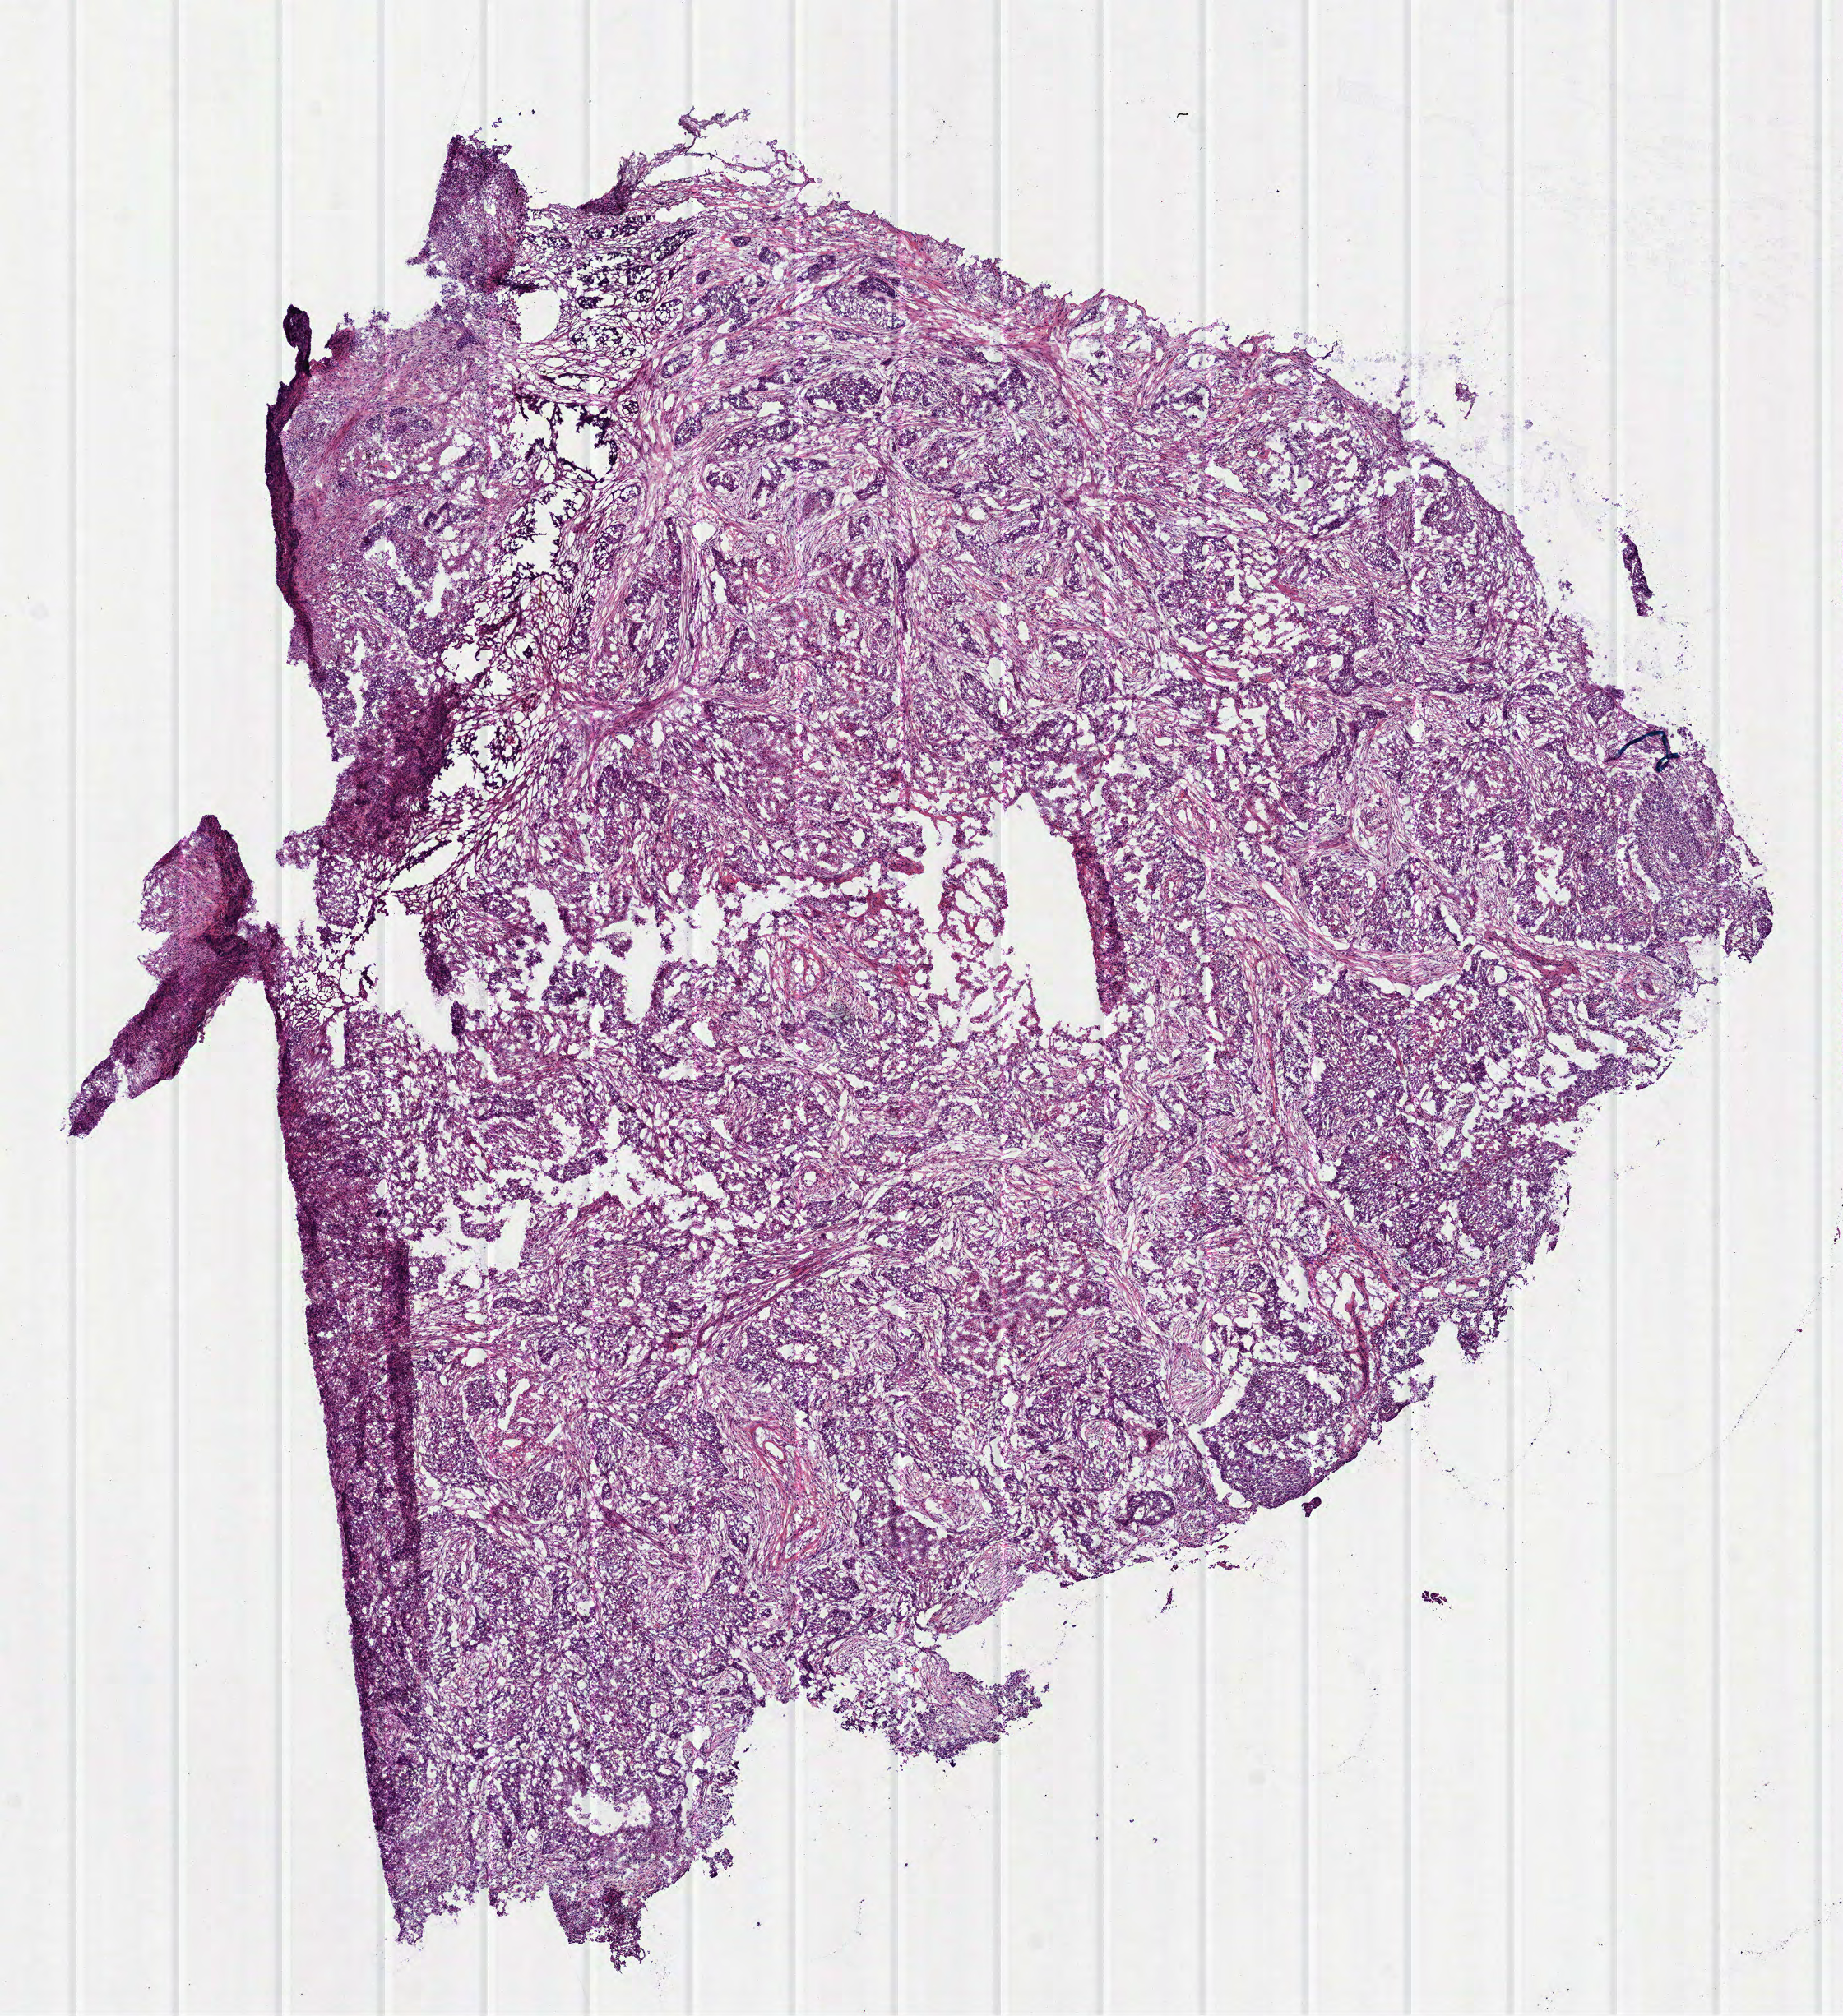
Digitized H&E-stained tissue section (whole slide), a low-resolution overview of the entire scanned area, about 9.0 x 9.9 mm (slide scanned at 40x); frozen section from the top of the tissue portion; sample: primary tumour, lung. Female, age 83 years at initial diagnosis. Slide review estimates, as recorded: tumour cells 93%, tumour nuclei 80%, normal cells 0%, stromal cells 0%, necrosis 7%. Inflammatory infiltration, as recorded: lymphocyte infiltration 2%, monocyte infiltration 0%, neutrophil infiltration 2%.
AJCC pathologic stage: IIB (7th edition). TNM: T2 N1 M0. Histologic diagnosis: Squamous cell carcinoma, NOS (lower lobe, lung).